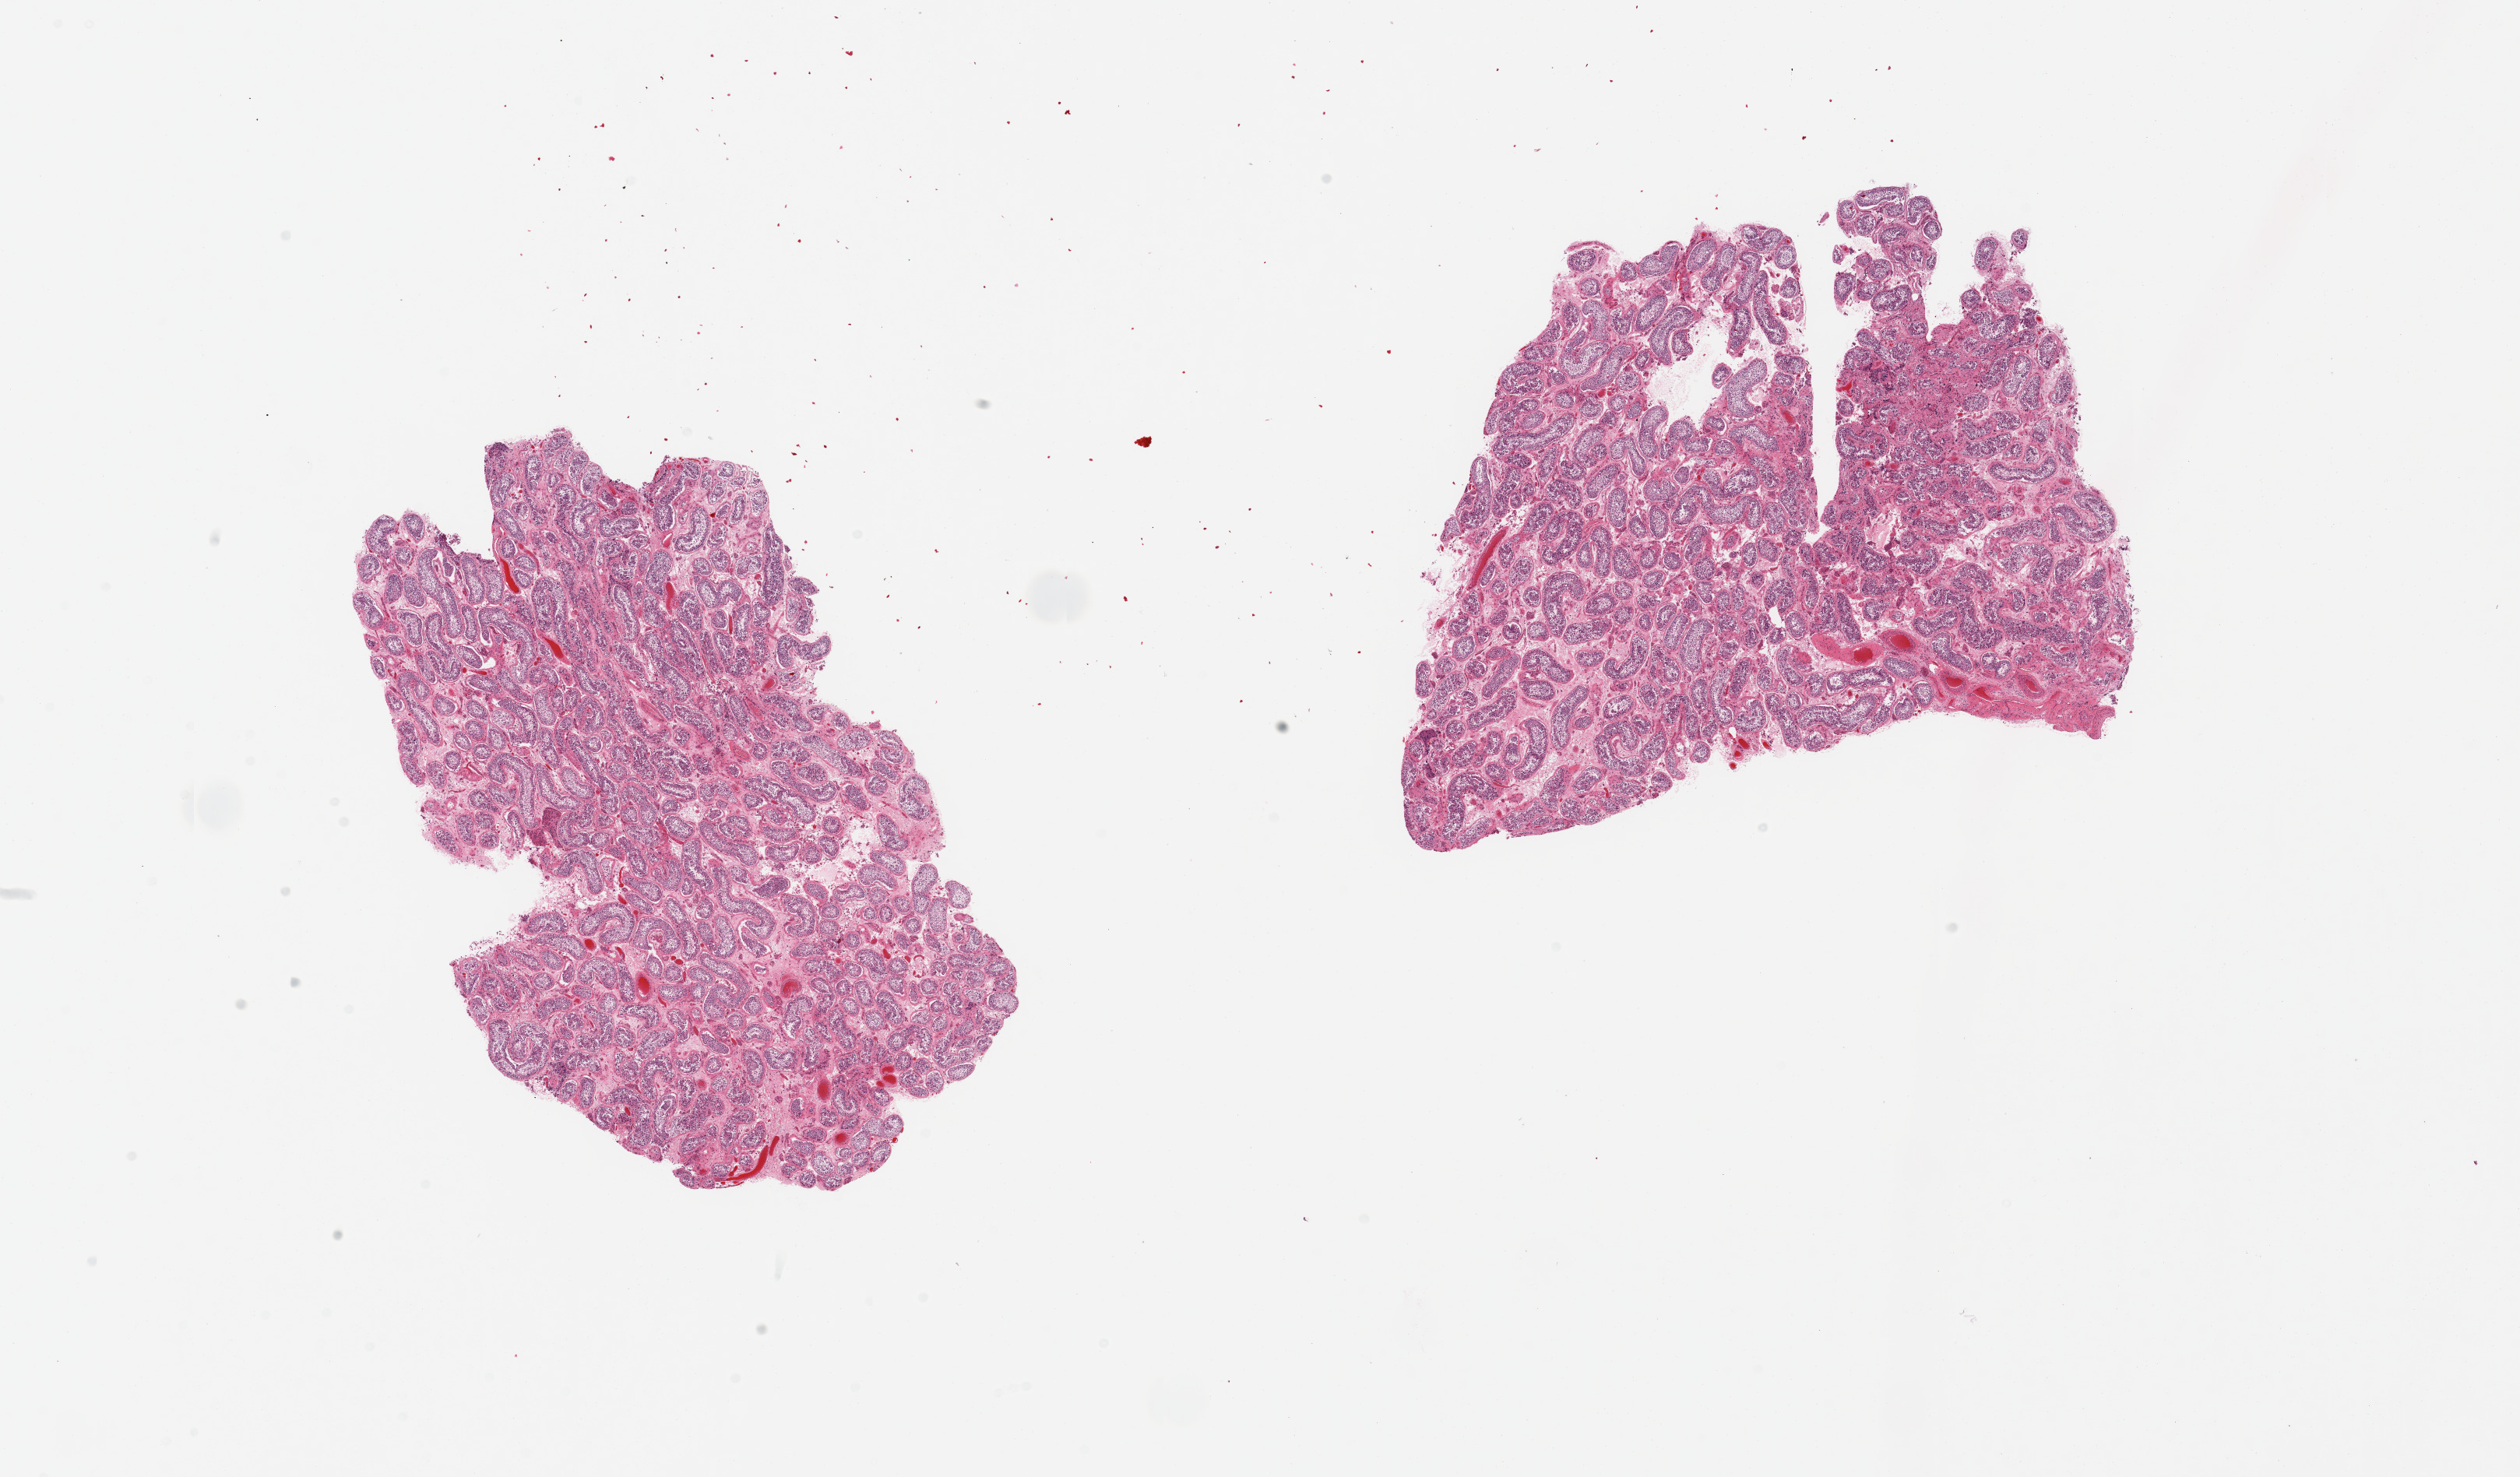
Digitized hematoxylin and eosin (H&E)-stained section, brightfield — shown as a low-resolution overview of the whole scanned area (about 25.6 x 15.0 mm, acquisition: 20x scan); PAXgene-fixed paraffin-embedded (PFPE) section; section of testis (target tissue); donor tissue sample. Donor: male.
Review note (as recorded): 2 pieces; active spermatogenesis.